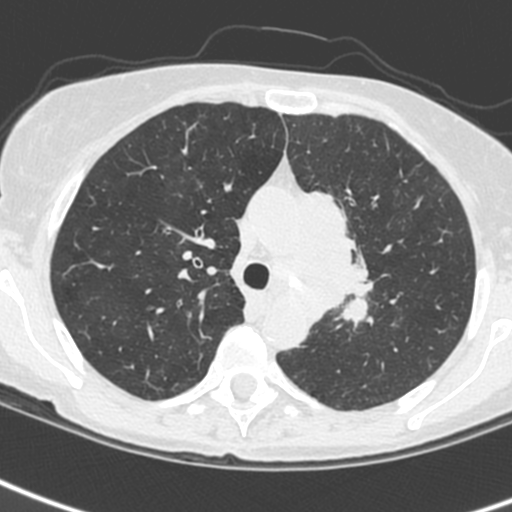
Low-dose screening chest CT, one axial slice; position 173 of 242 along the scan axis; 120 kVp; lung window (W 1500 / L -600 HU); 512 × 512 image matrix, field of view 284 × 284 mm.
Annotated regions visible in this slice (outlined manually by an expert reader):
- lesion 3 (tumor, upper lobe of left lung): bounding box <303,191,370,321> (left, top, right, bottom; pixels)